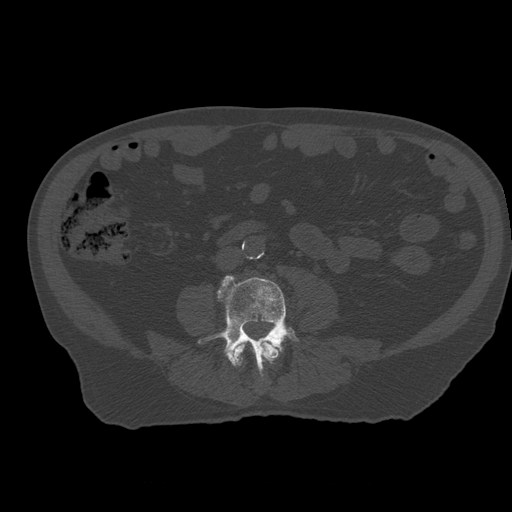
CT including the spine, one axial slice; slice 169 of 399 in the series (ordered by position); reconstruction kernel STANDARD; bone window (W 1800 / L 400 HU); 1.25 mm slice thickness; 512 × 512 image matrix, field of view 407 × 407 mm. Patient age 73 years. From the clinical record (not read from this slice): primary cancer: prostate; vertebrae with lytic lesions (as recorded): L2.
Structures marked on this image (semi-automatically segmented with operator editing):
- L3 vertebra: bounding box [x1, y1, x2, y2] px = [235, 341, 279, 365]
- L4 vertebra: [198, 275, 300, 372]